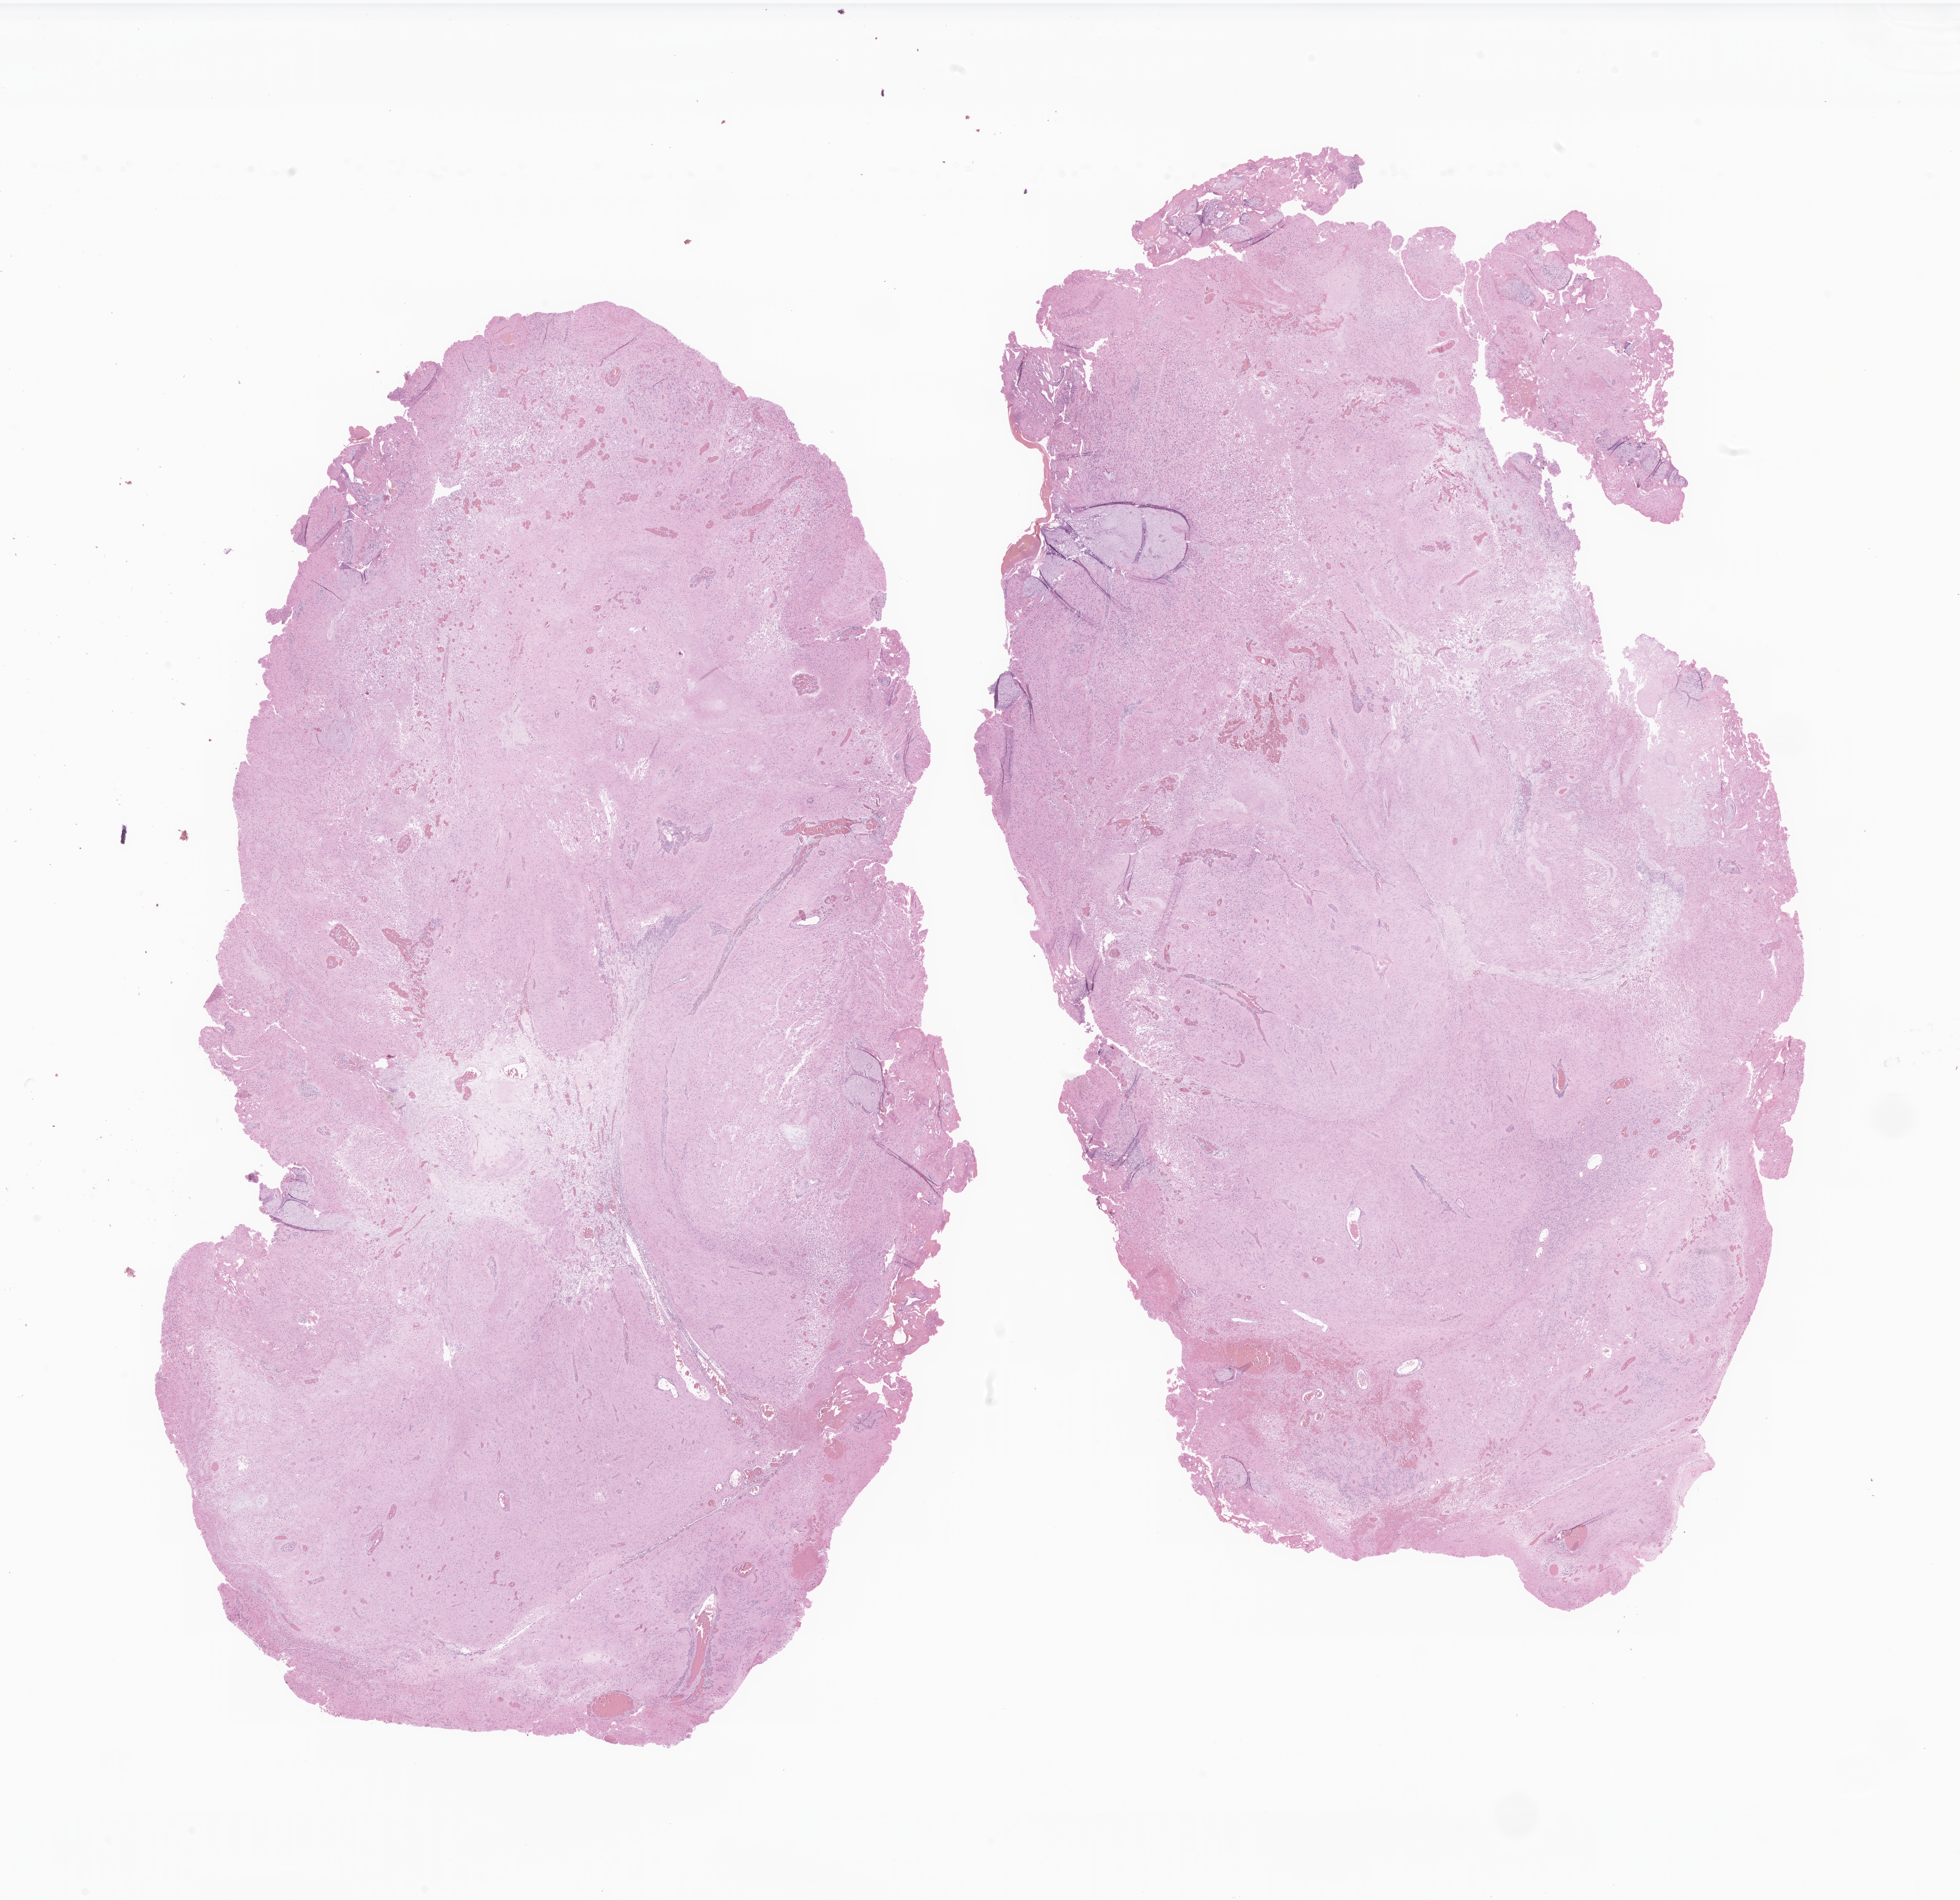
Digitized hematoxylin and eosin (H&E)-stained section of tumor tissue from the brain, a low-resolution overview of the entire scanned area, about 23.3 x 22.6 mm. FFPE section. Patient: male, age 136 months (11 years 4 months).
Diagnosis (ICD-O-3 morphology term): Glioma, malignant.